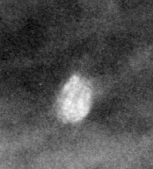
Cropped region of a digitized screen-film mammogram centred on a radiologist-marked abnormality; right breast; CC view.
- Calcifications, morphology round and regular / eggshell; BI-RADS assessment category 2; subtlety rating 3 on a 1 (subtle) to 5 (obvious) scale; benign without callback (not worked up further).